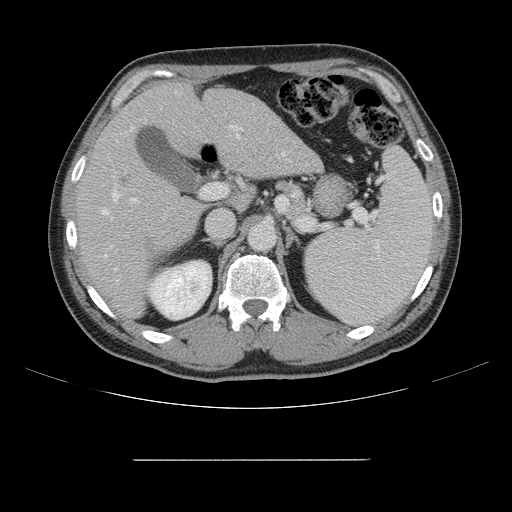
Contrast-enhanced abdominal CT, one axial slice. Intravenous contrast given. Soft-tissue window (W 400 / L 40 HU). 2.5 mm slice thickness. 512 × 512 image matrix. Male patient, age 54 years. Case-level facts recorded for this patient, not image findings: diagnosis: colorectal cancer liver metastases, imaged before liver resection; multiple liver metastases: yes; largest metastasis: 1 cm; chemotherapy before resection: yes.
Structures marked on this image (expert manual segmentation):
- hepatic veins: bounding box <103,133,284,283> (left, top, right, bottom; pixels)
- liver: <78,82,319,318>
- planned liver remnant (the part of the liver to remain after resection): <77,83,233,317>
- portal vein (with intrahepatic branches): <130,119,240,203>